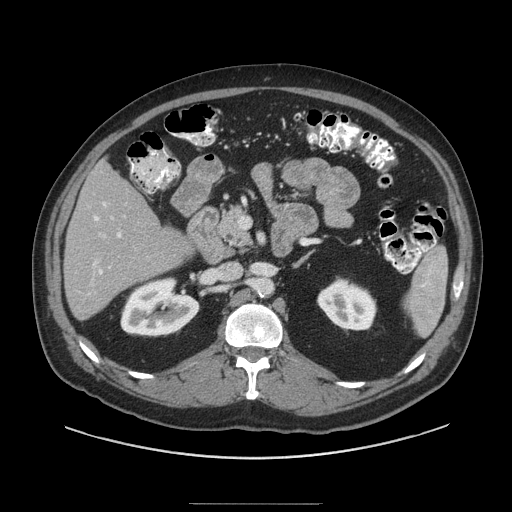
Contrast-enhanced abdominal CT (liver protocol), one axial slice. Soft-tissue window (W 400 / L 40 HU). 512 × 512 image matrix, field of view 440 × 440 mm. From the clinical record (not read from this slice): diagnosis: hepatocellular carcinoma (patient treated with transarterial chemoembolisation; whether this scan precedes or follows treatment is not stated here); TNM stage (as recorded): Stage-I; Child-Pugh class: A; tumour differentiation: well differentiated; tumour nodularity: uninodular.
Outlined on this slice (semi-automatic segmentation, software-assisted and operator-edited):
- liver parenchyma outside the tumour (the mass and vessels are separate outlines, so this box may not span the whole liver): bounding box [x1, y1, x2, y2] px = [64, 162, 190, 320]
- liver vessels: [93, 202, 121, 274]